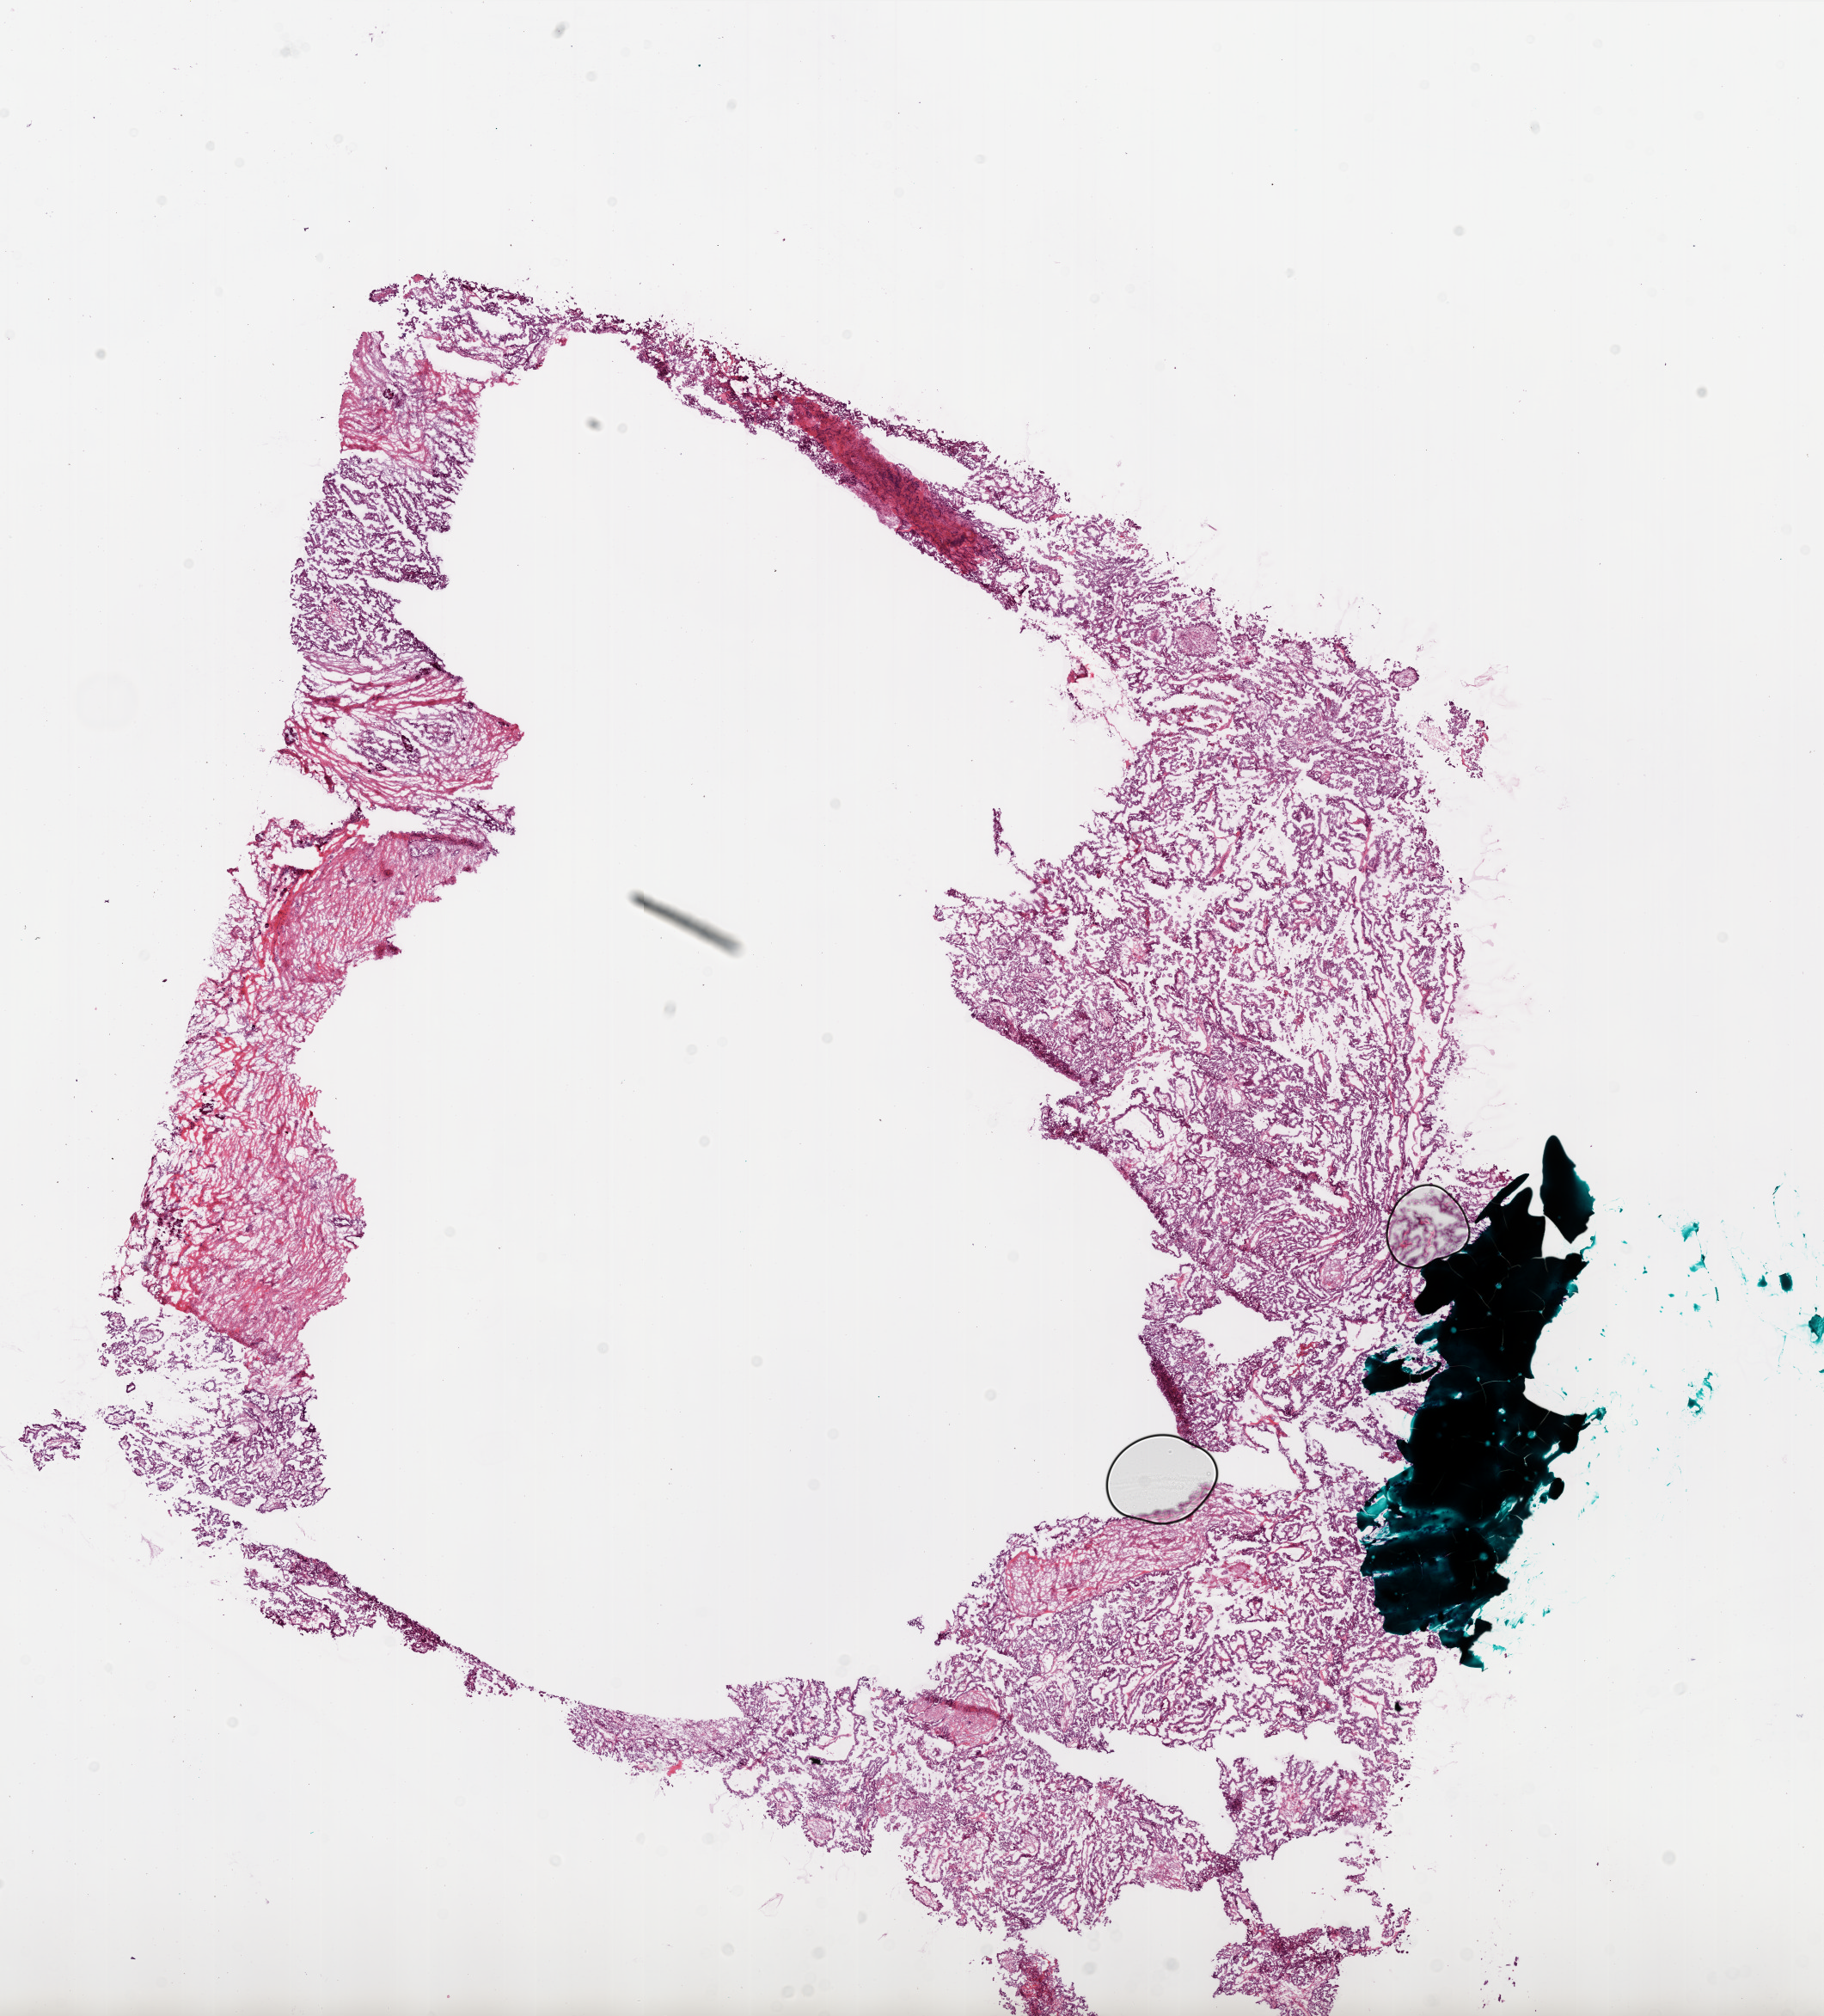
H&E-stained whole-slide image — a low-resolution overview of the entire scanned area, about 17.0 x 18.8 mm, frozen section from the bottom of the tissue portion, primary tumour sample from the ovary. Female, age 60 years at initial diagnosis. Pathologist review of this section (percent, as recorded): tumour cells 79%, tumour nuclei 80%.
Diagnosis: Serous cystadenocarcinoma, NOS.